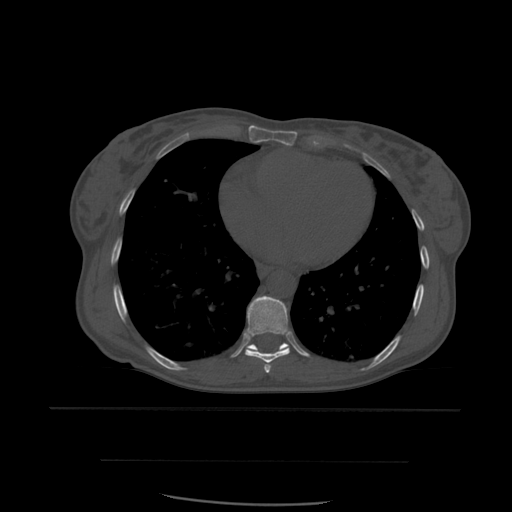
CT including the spine, one axial slice. Position 351 of 574 along the scan axis. Bone window (W 1800 / L 400 HU). 512 × 512 image matrix, field of view 392 × 392 mm. Patient age 48 years. Case-level facts recorded for this patient, not image findings: primary cancer: lung.
Annotated regions visible in this slice (semi-automatic segmentation, software-assisted and operator-edited):
- T7 vertebra: bounding box <265,366,271,373> (left, top, right, bottom; pixels)
- T8 vertebra: <245,296,290,372>
- T9 vertebra: <246,338,290,352>